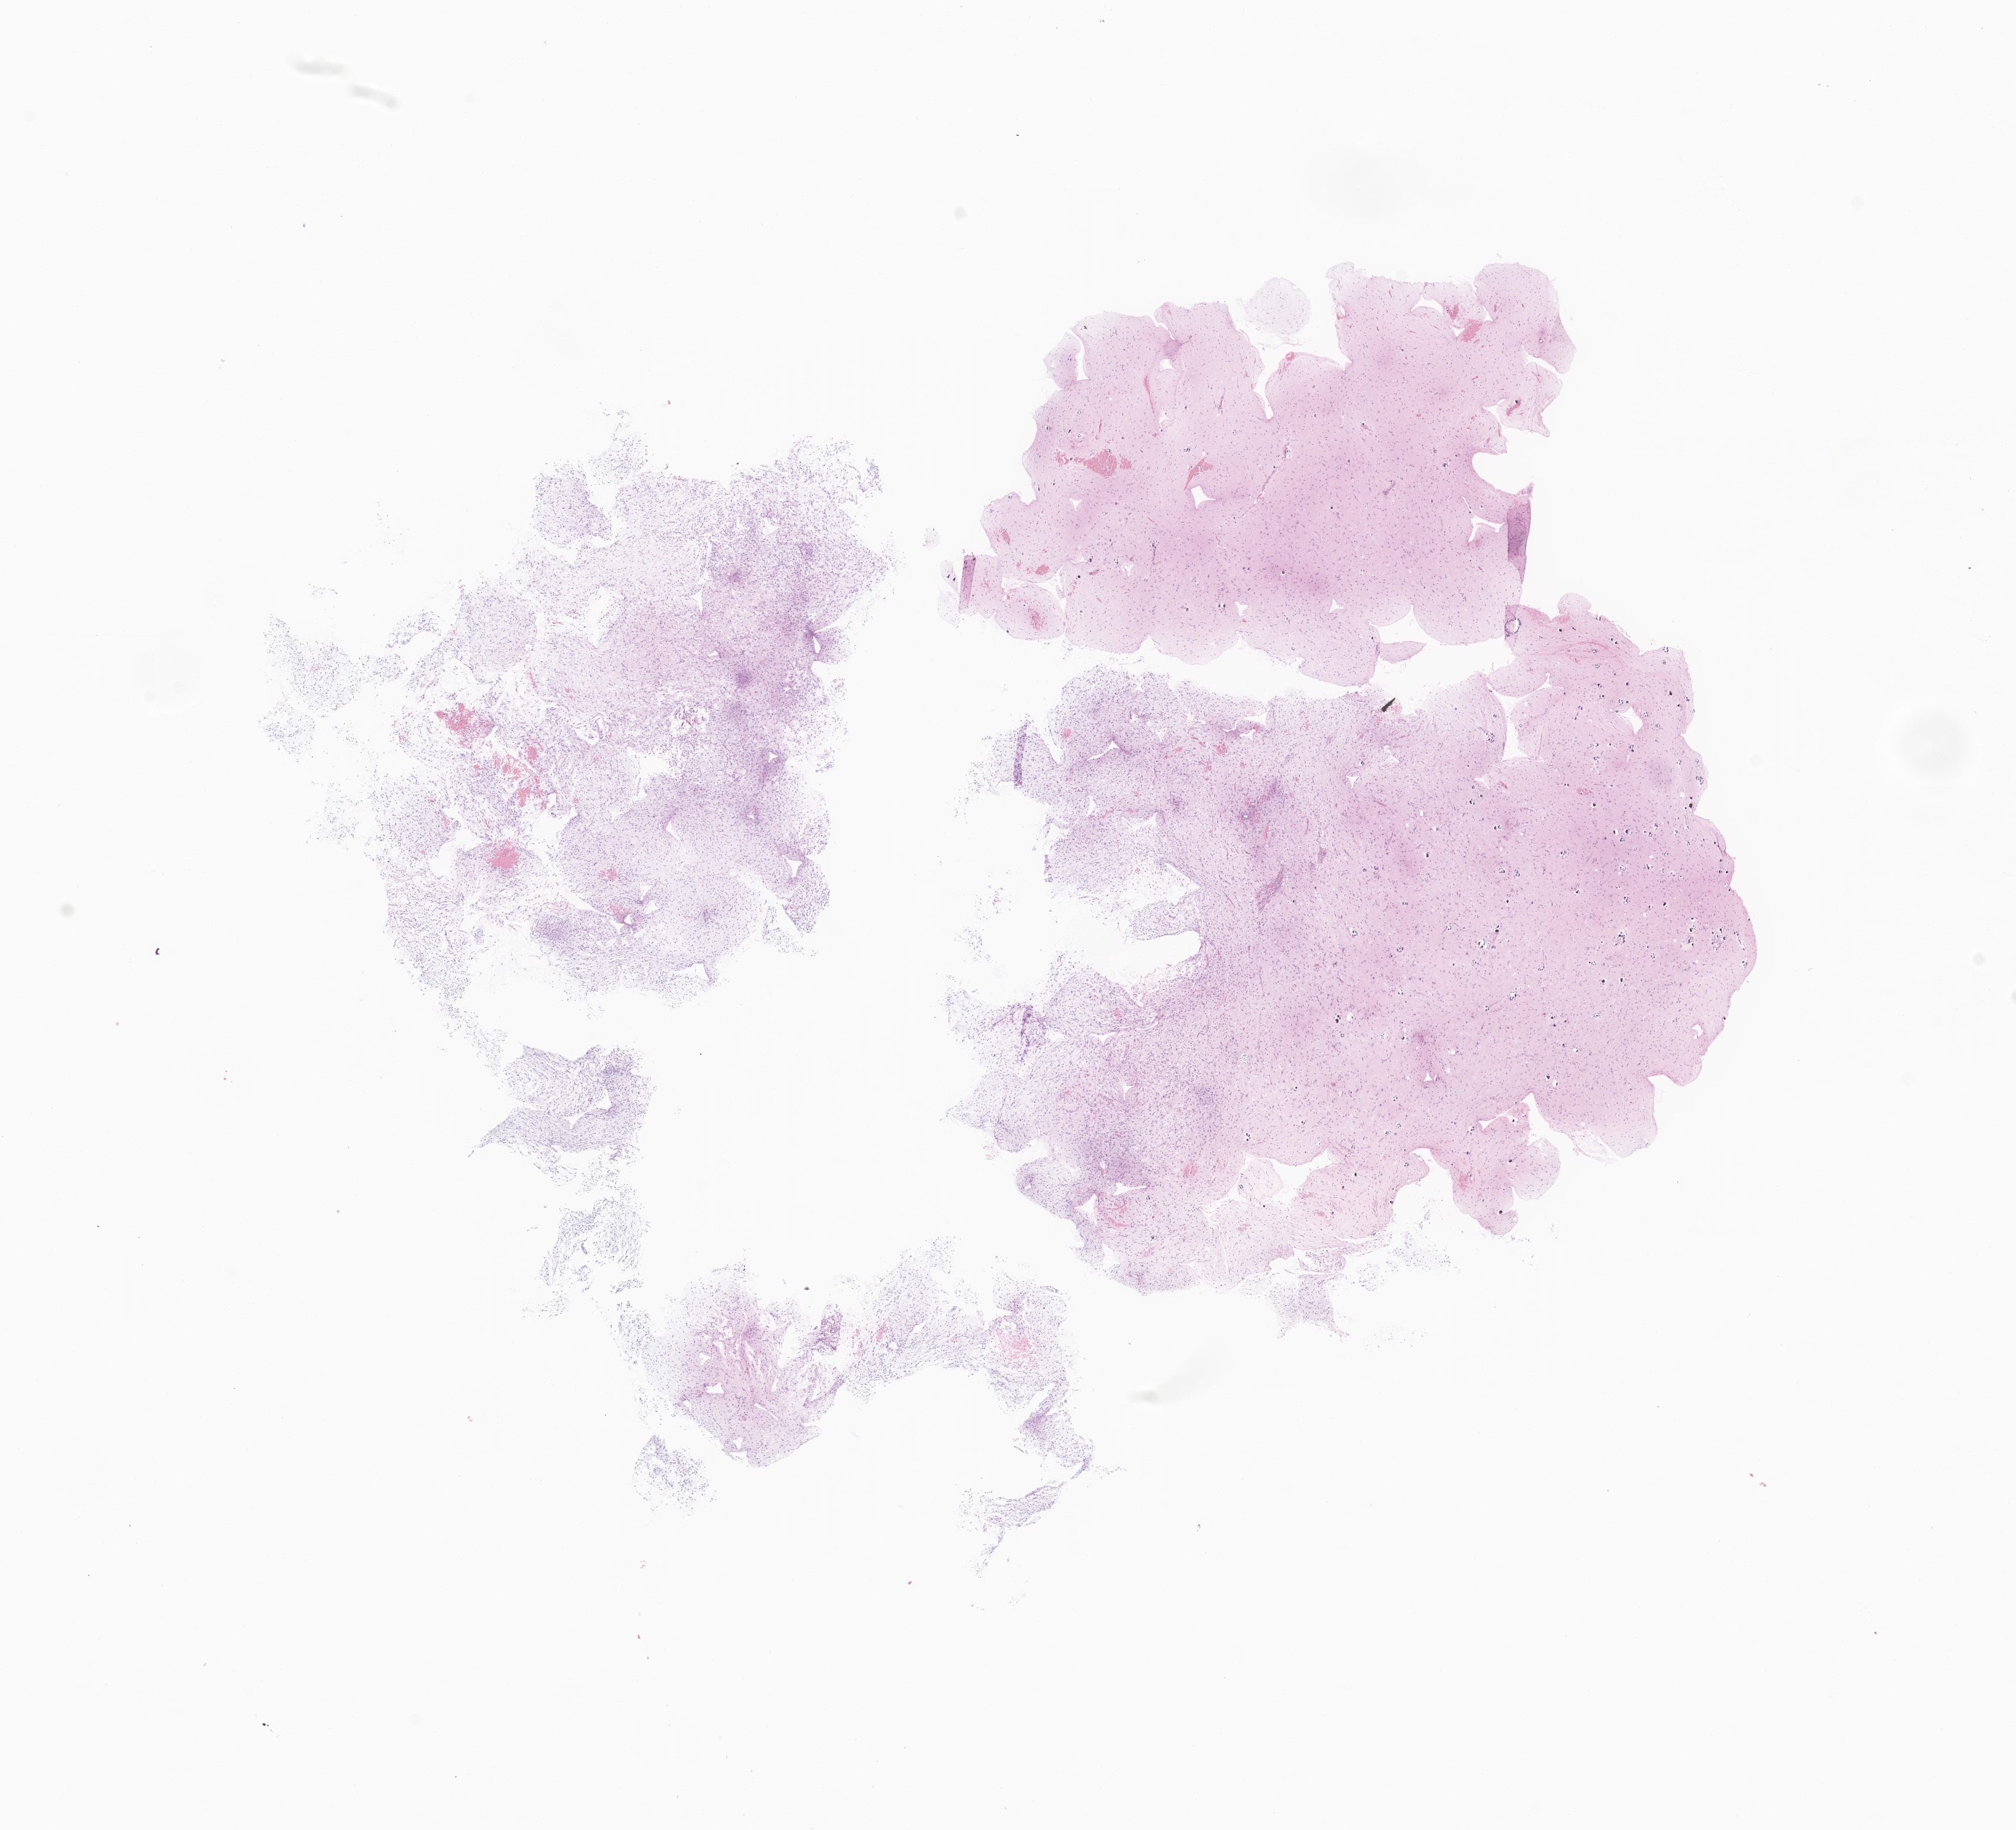
Digitized hematoxylin and eosin (H&E)-stained section of tumor tissue from the brain — a low-resolution overview of the entire scanned area, about 14.4 x 13.1 mm. Formalin-fixed paraffin-embedded section. Male patient, age 373 days (about 1.0 years).
Diagnosis: Oligoastrocytoma, NOS.